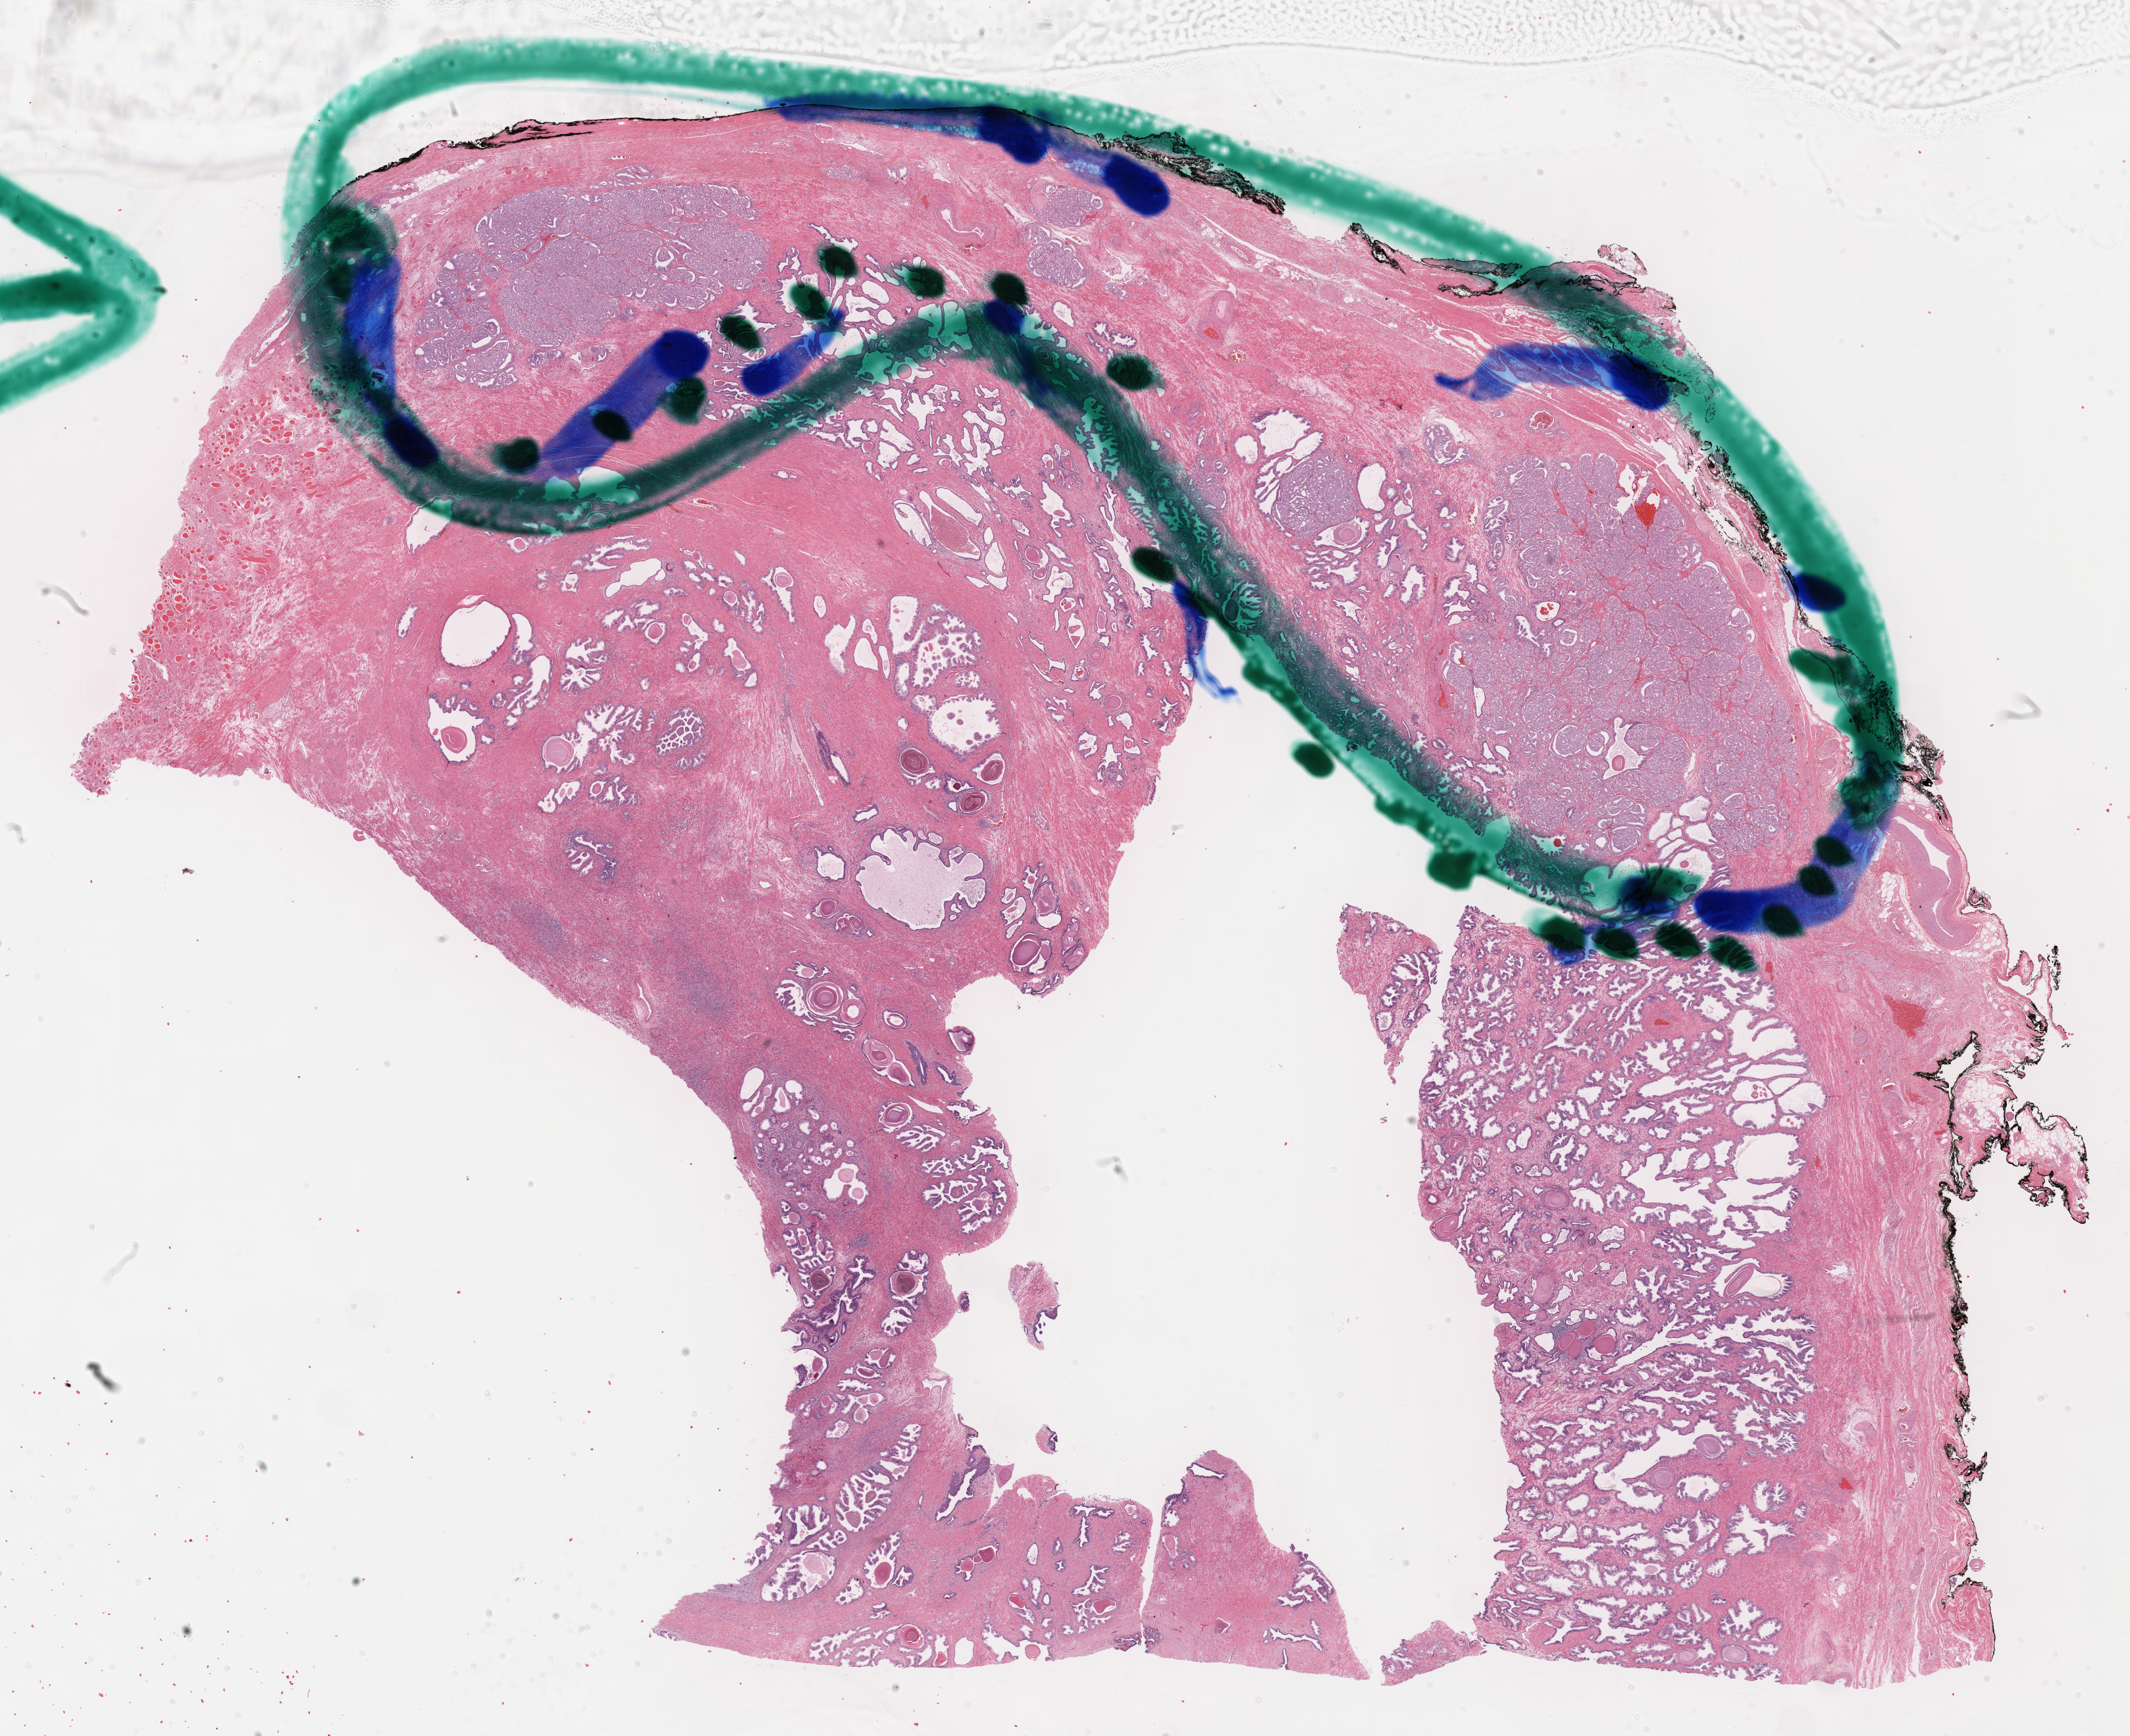
Whole-slide histology image, Hematoxylin and eosin (H&E) stained — low-resolution overview of the scanned area, about 26.2 x 21.3 mm (acquisition: 40x scan); frozen section; sample: primary tumour, prostate. Male, age 65 years at initial diagnosis. Gleason score: 7 (4+3). Pathologist review of this section (percent, as recorded): tumour cells 50%, tumour nuclei 60%, normal cells 10%, stromal cells 40%, necrosis 0%. Infiltration values recorded for this section: lymphocyte infiltration 0%, monocyte infiltration 0%, neutrophil infiltration 0%.
Pathologic diagnosis: Adenocarcinoma, NOS (prostate gland).